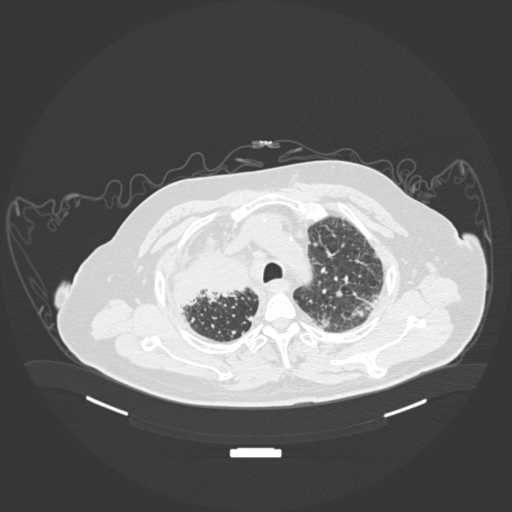
Chest CT, one axial slice; position 150 of 201 along the scan axis; reconstruction kernel B30f; lung window (W 1500 / L -600 HU); 1 mm slice thickness; 512 × 512 image matrix, field of view 500 × 500 mm. Male patient, age 69 years. From the clinical record (not read from this slice): clinical TNM (as recorded): T4 N3 M1.
Annotated regions visible in this slice (rectangle marked by the reading radiologist):
- lung tumour (recorded histology: adenocarcinoma): box from (x=165, y=231) to (x=256, y=312) px